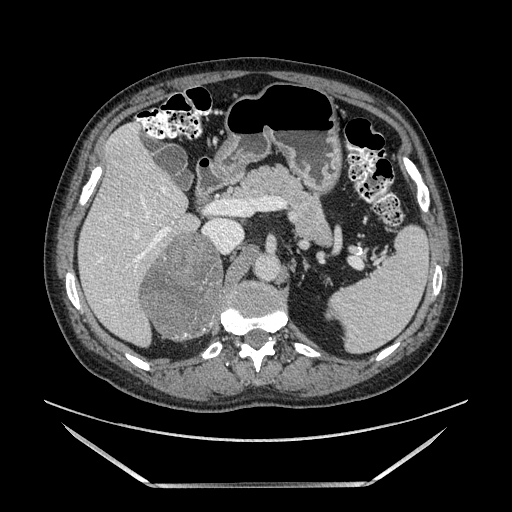
Contrast-enhanced abdominal CT, one axial slice. Slice 86 of 185 in the series (ordered by position). Soft-tissue window (W 400 / L 40 HU). 1.25 mm slice thickness. 512 × 512 image matrix. Male patient. Case-level facts recorded for this patient, not image findings: diagnosis: adrenocortical carcinoma; tumour side: right adrenal.
Outlined on this slice (semi-automatically segmented with operator editing):
- mass: bounding box [x1, y1, x2, y2] px = [143, 231, 224, 337]